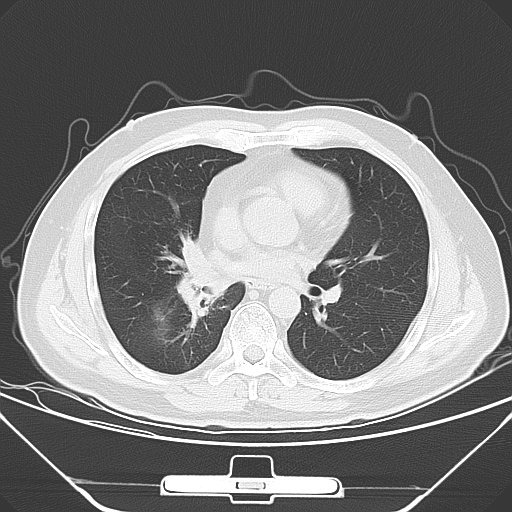
Chest CT, one axial slice. Position 27 of 56 along the scan axis. 120 kVp. Lung window (W 1500 / L -600 HU). 512 × 512 image matrix, field of view 371 × 371 mm. Male patient, age 48 years. Case-level facts recorded for this patient, not image findings: clinical TNM (as recorded): T1a N1 M1c; histopathological grade: G3.
Annotated regions visible in this slice (bounding box drawn by a radiologist):
- lung tumour (recorded histology: adenocarcinoma): bounding box <170,230,222,322> (left, top, right, bottom; pixels)